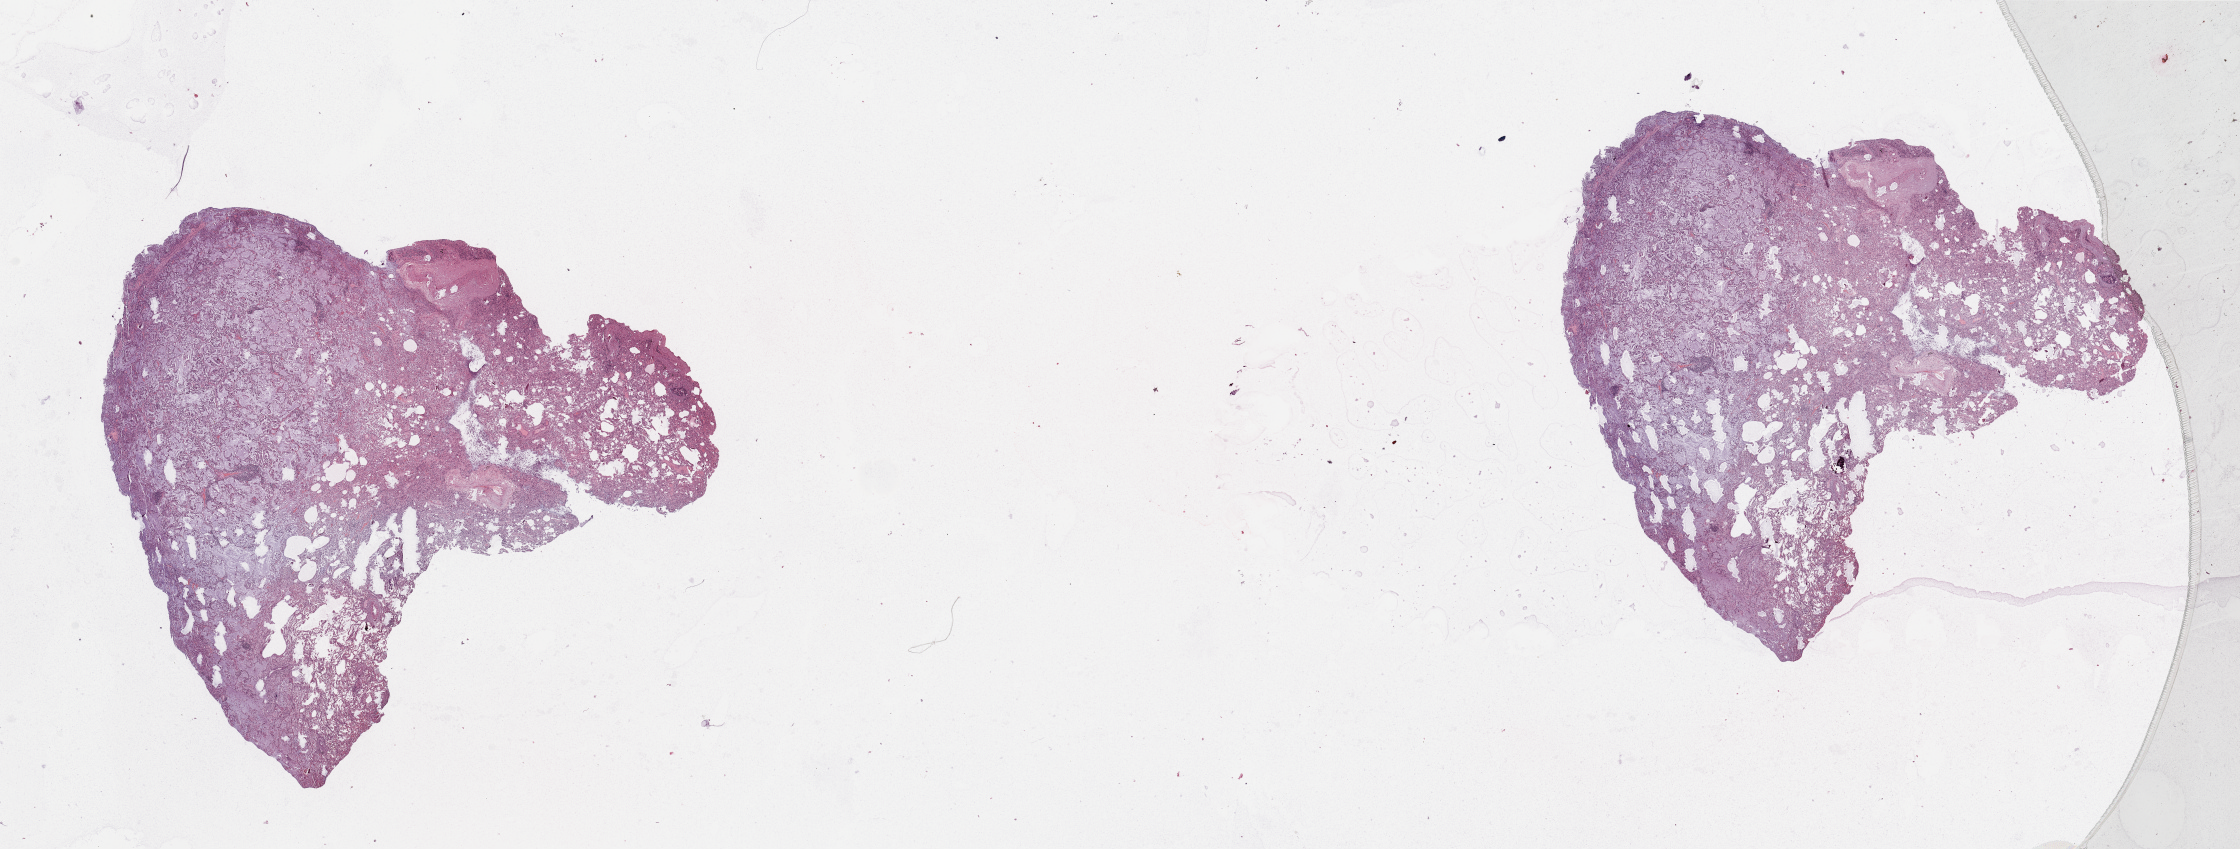
H&E whole-slide image — shown as a low-resolution overview of the whole scanned area (about 35.4 x 13.4 mm), tumour tissue sample, sampled site: lung. Patient: male, age 67 years.
Diagnosis: Adenocarcinoma, NOS.